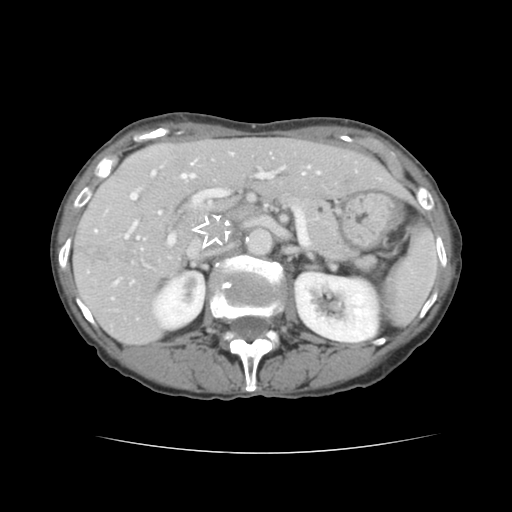
Contrast-enhanced abdominal CT, one axial slice. Position 80 of 136 along the scan axis. Intravenous contrast given. Soft-tissue window (W 400 / L 40 HU). 2.5 mm slice thickness. 512 × 512 image matrix, field of view 319 × 319 mm. Female patient, age 77 years. Case-level facts recorded for this patient, not image findings: diagnosis: colorectal cancer liver metastases, imaged before liver resection; multiple liver metastases: yes.
Structures marked on this image (expert manual segmentation):
- hepatic veins: bounding box (x1, y1, x2, y2) in pixels: (137, 163, 320, 239)
- liver: (75, 138, 408, 344)
- planned liver remnant (the part of the liver to remain after resection): (154, 138, 407, 202)
- portal vein (with intrahepatic branches): (95, 161, 283, 284)